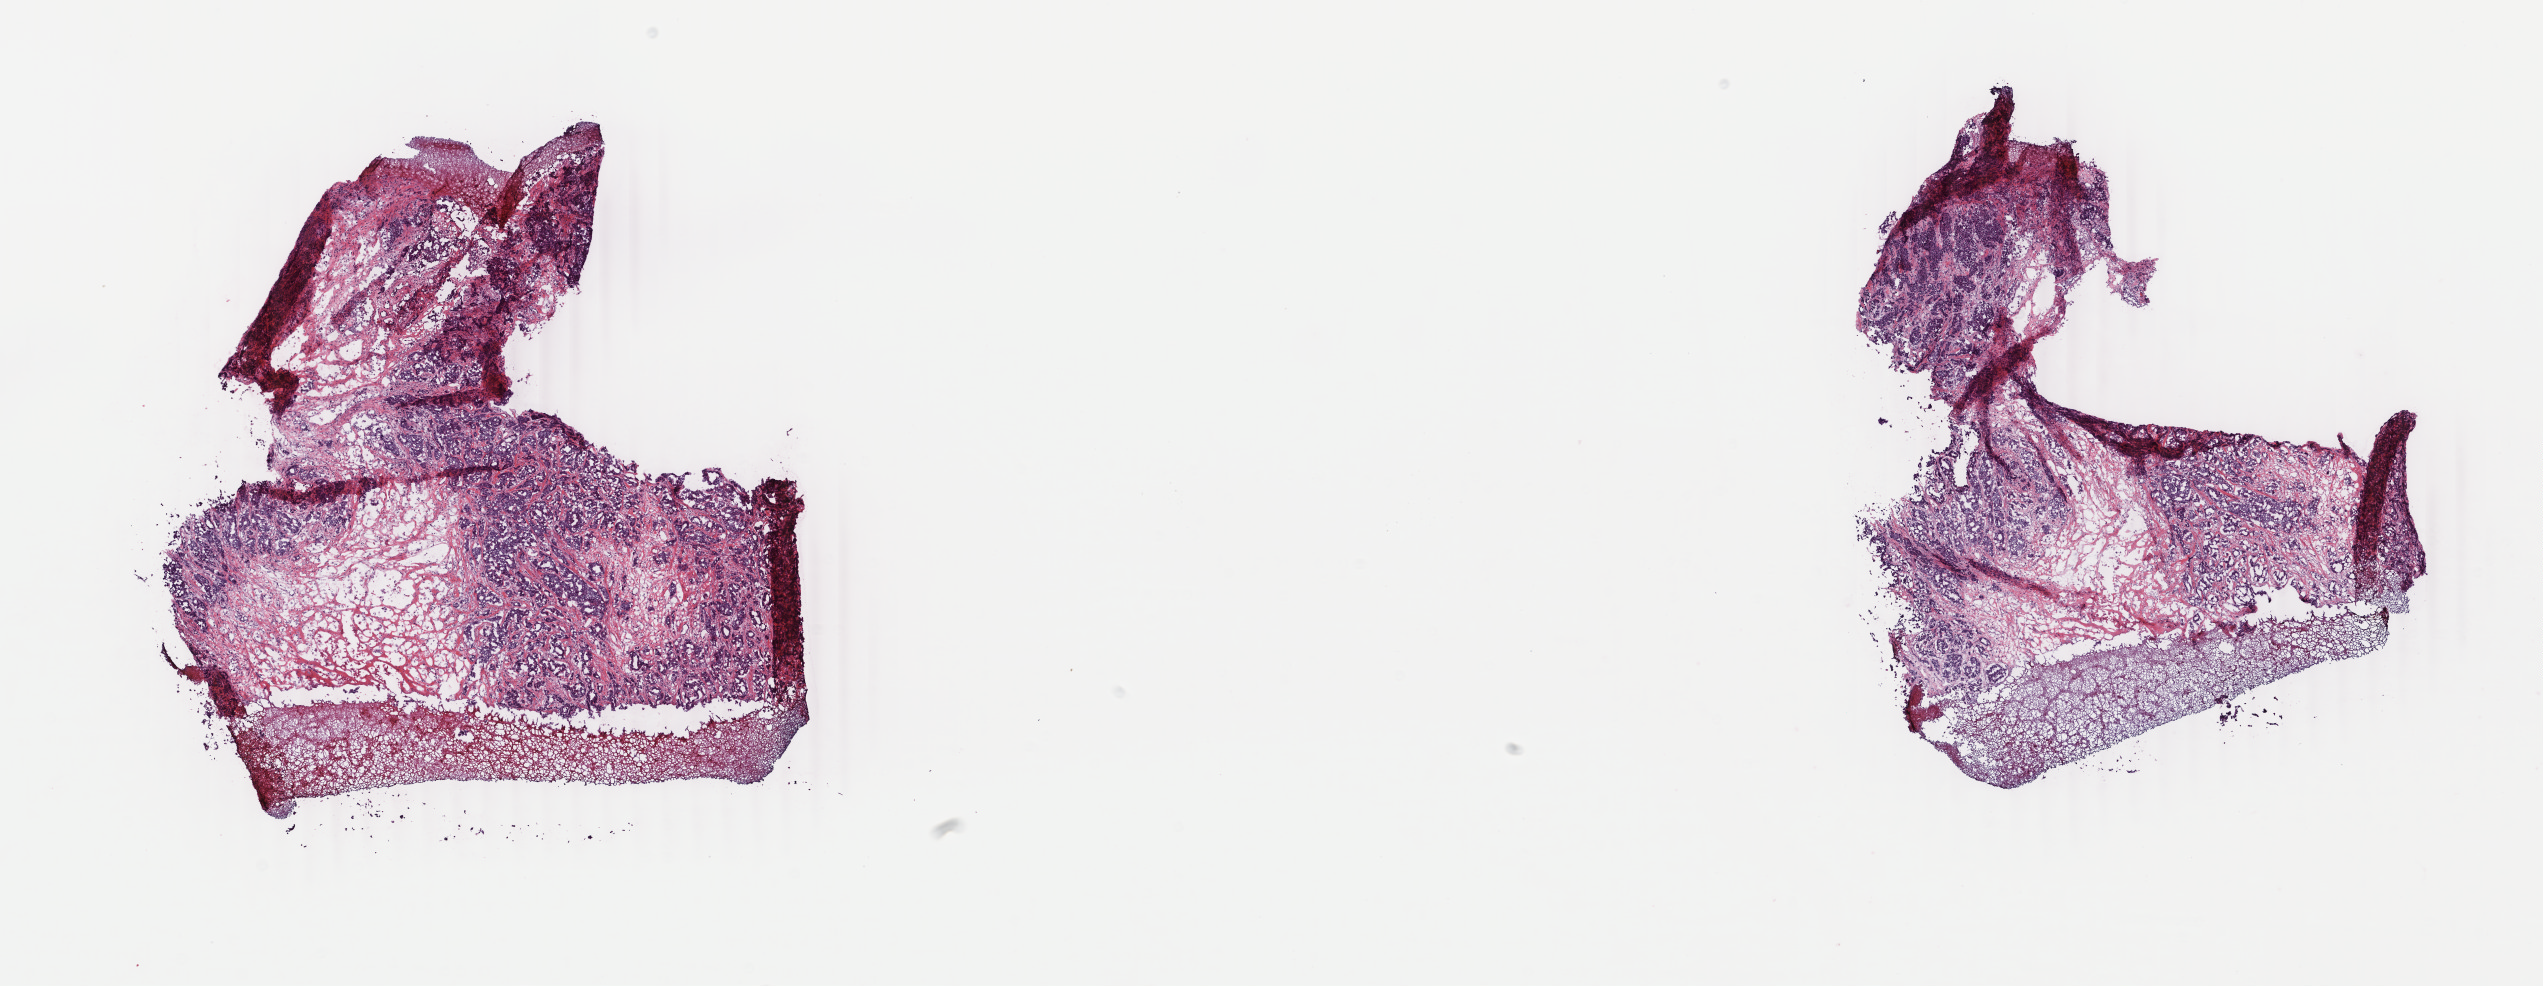
H&E-stained whole-slide image, low-resolution overview of the scanned area, about 20.2 x 7.8 mm (from a 40x scan); frozen section from the top of the tissue portion; sample: primary tumour, breast. Patient: female, age at initial diagnosis 26 years. Pathologist review of this section (percent, as recorded): tumour cells 40%, tumour nuclei 80%, normal cells 0%, stromal cells 50%, necrosis 10%. Inflammatory infiltration, as recorded: lymphocyte infiltration 0%, monocyte infiltration 0%, neutrophil infiltration 0%.
Diagnosis: Infiltrating duct carcinoma, NOS. TNM: T3 N0 (i-) M0. AJCC pathologic stage: IIB (4th edition). Laterality: left.